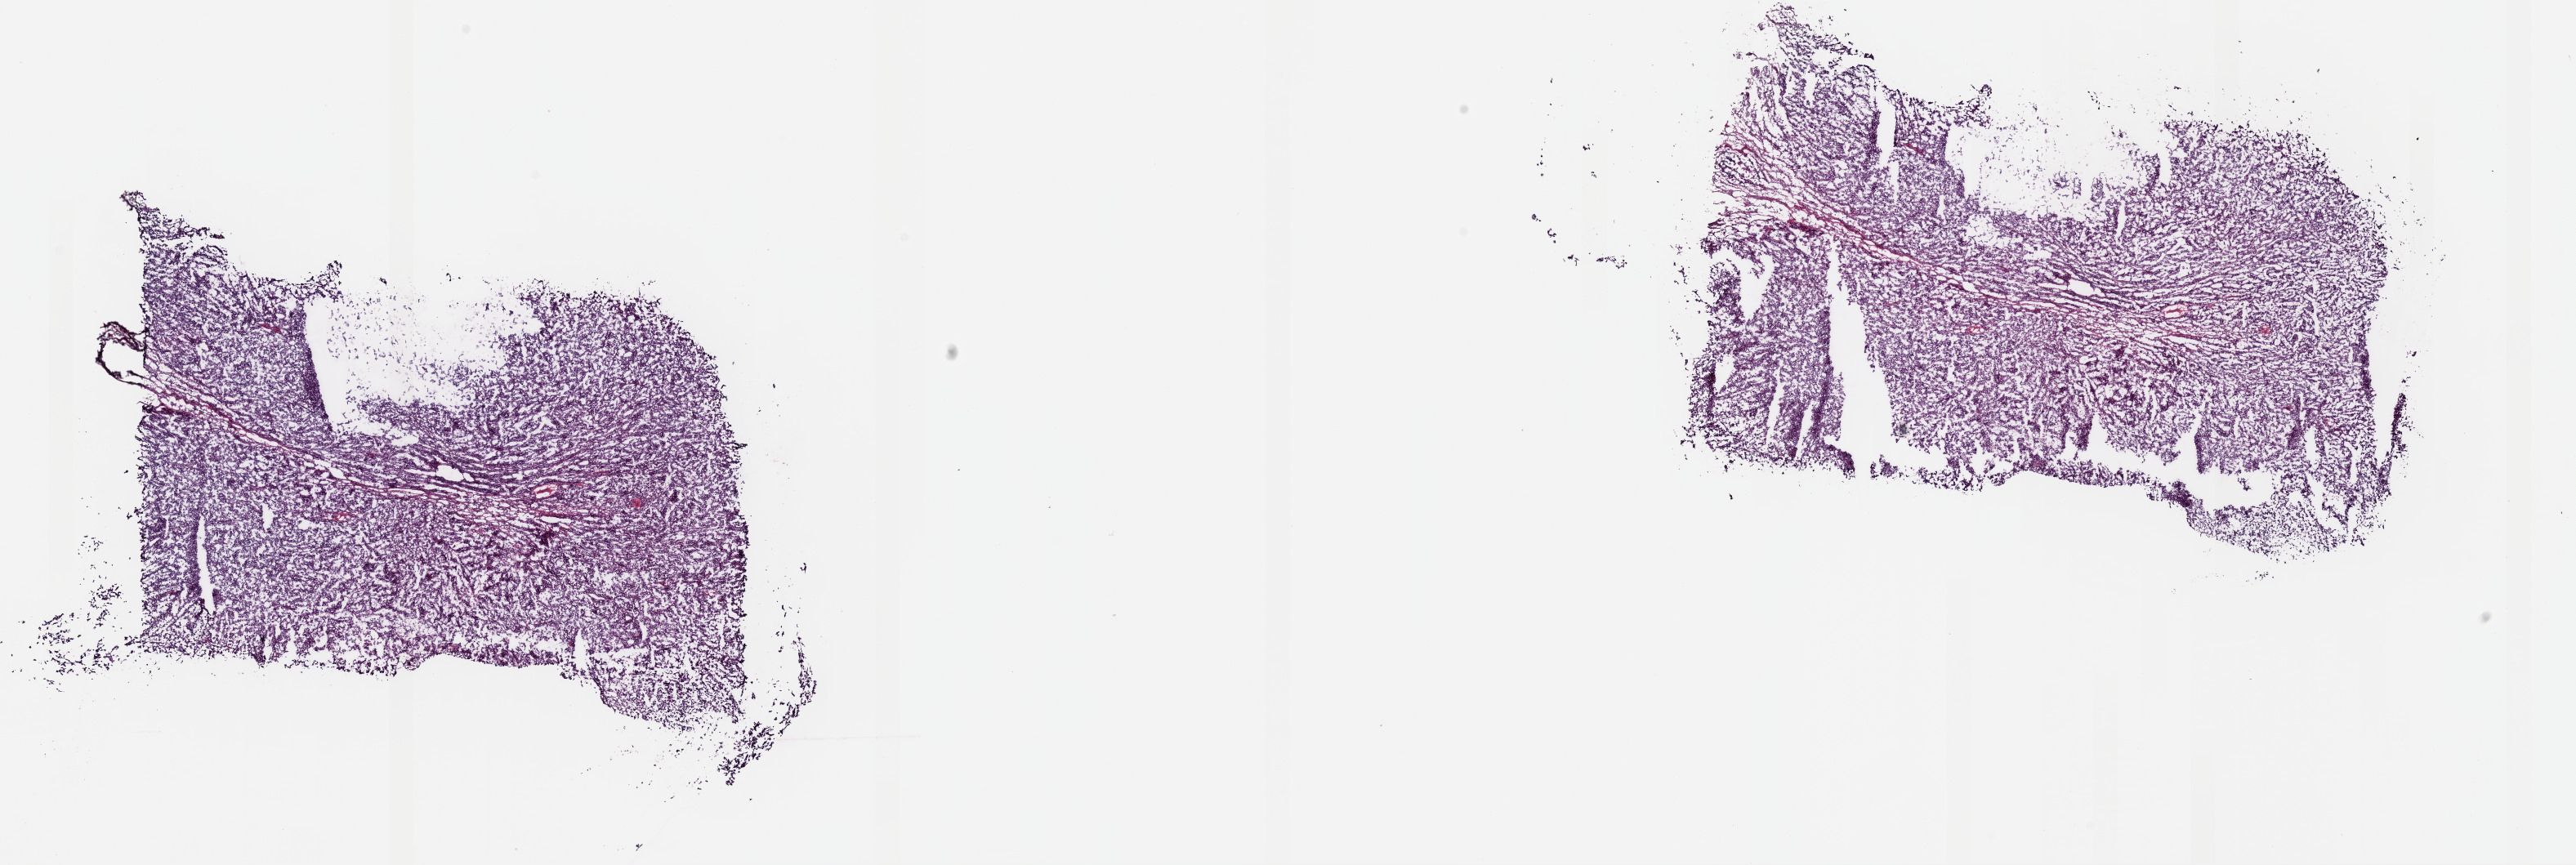
Whole-slide histology image, Hematoxylin and eosin (H&E) stained — low-resolution overview of the scanned area, about 24.9 x 8.4 mm. Frozen section from the top of the tissue portion. Metastatic tumour sample. Patient sex: female. Composition of this section per pathologist review: tumour cells 95%, tumour nuclei 95%, normal cells 3%, stromal cells 1%, necrosis 1%. Inflammatory infiltration, as recorded: lymphocyte infiltration 1%, monocyte infiltration 2%, neutrophil infiltration 0%.
This section: metastatic tumour tissue. Patient diagnosis: Malignant melanoma, NOS.